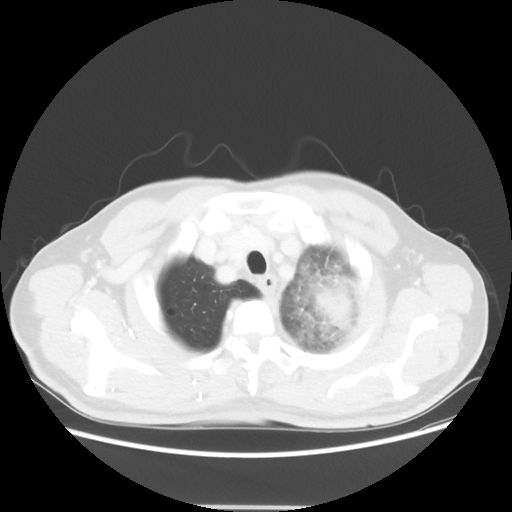
Chest CT, one axial slice. 100 kVp. Lung window (W 1500 / L -600 HU). 5 mm slice thickness. 512 × 512 image matrix, field of view 391 × 391 mm. Male patient, age 60 years. Case-level facts recorded for this patient, not image findings: clinical TNM (as recorded): T4 N1 M1a; histopathological grade: G3.
Outlined on this slice (bounding box drawn by a radiologist):
- lung tumour (recorded histology: large cell carcinoma): bounding box [x1, y1, x2, y2] px = [309, 276, 367, 338]